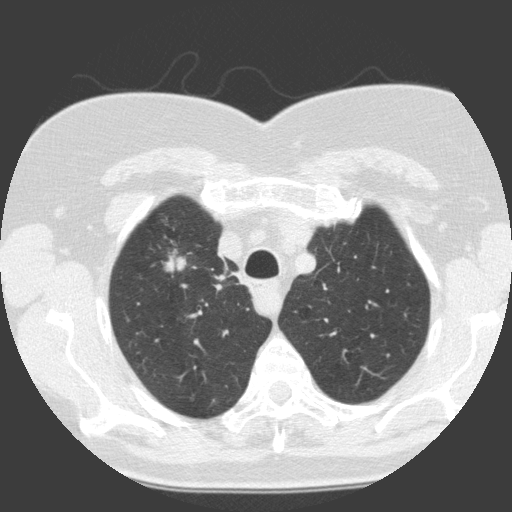
Low-dose screening chest CT, one axial slice; position 119 of 146 along the scan axis; 120 kVp; lung window (W 1500 / L -600 HU); 2 mm slice thickness; 512 × 512 image matrix, field of view 300 × 300 mm.
Outlined on this slice (manually delineated by an expert):
- lesion 1 (tumor, upper lobe of right lung): bounding box (x1, y1, x2, y2) in pixels: (162, 251, 187, 277)